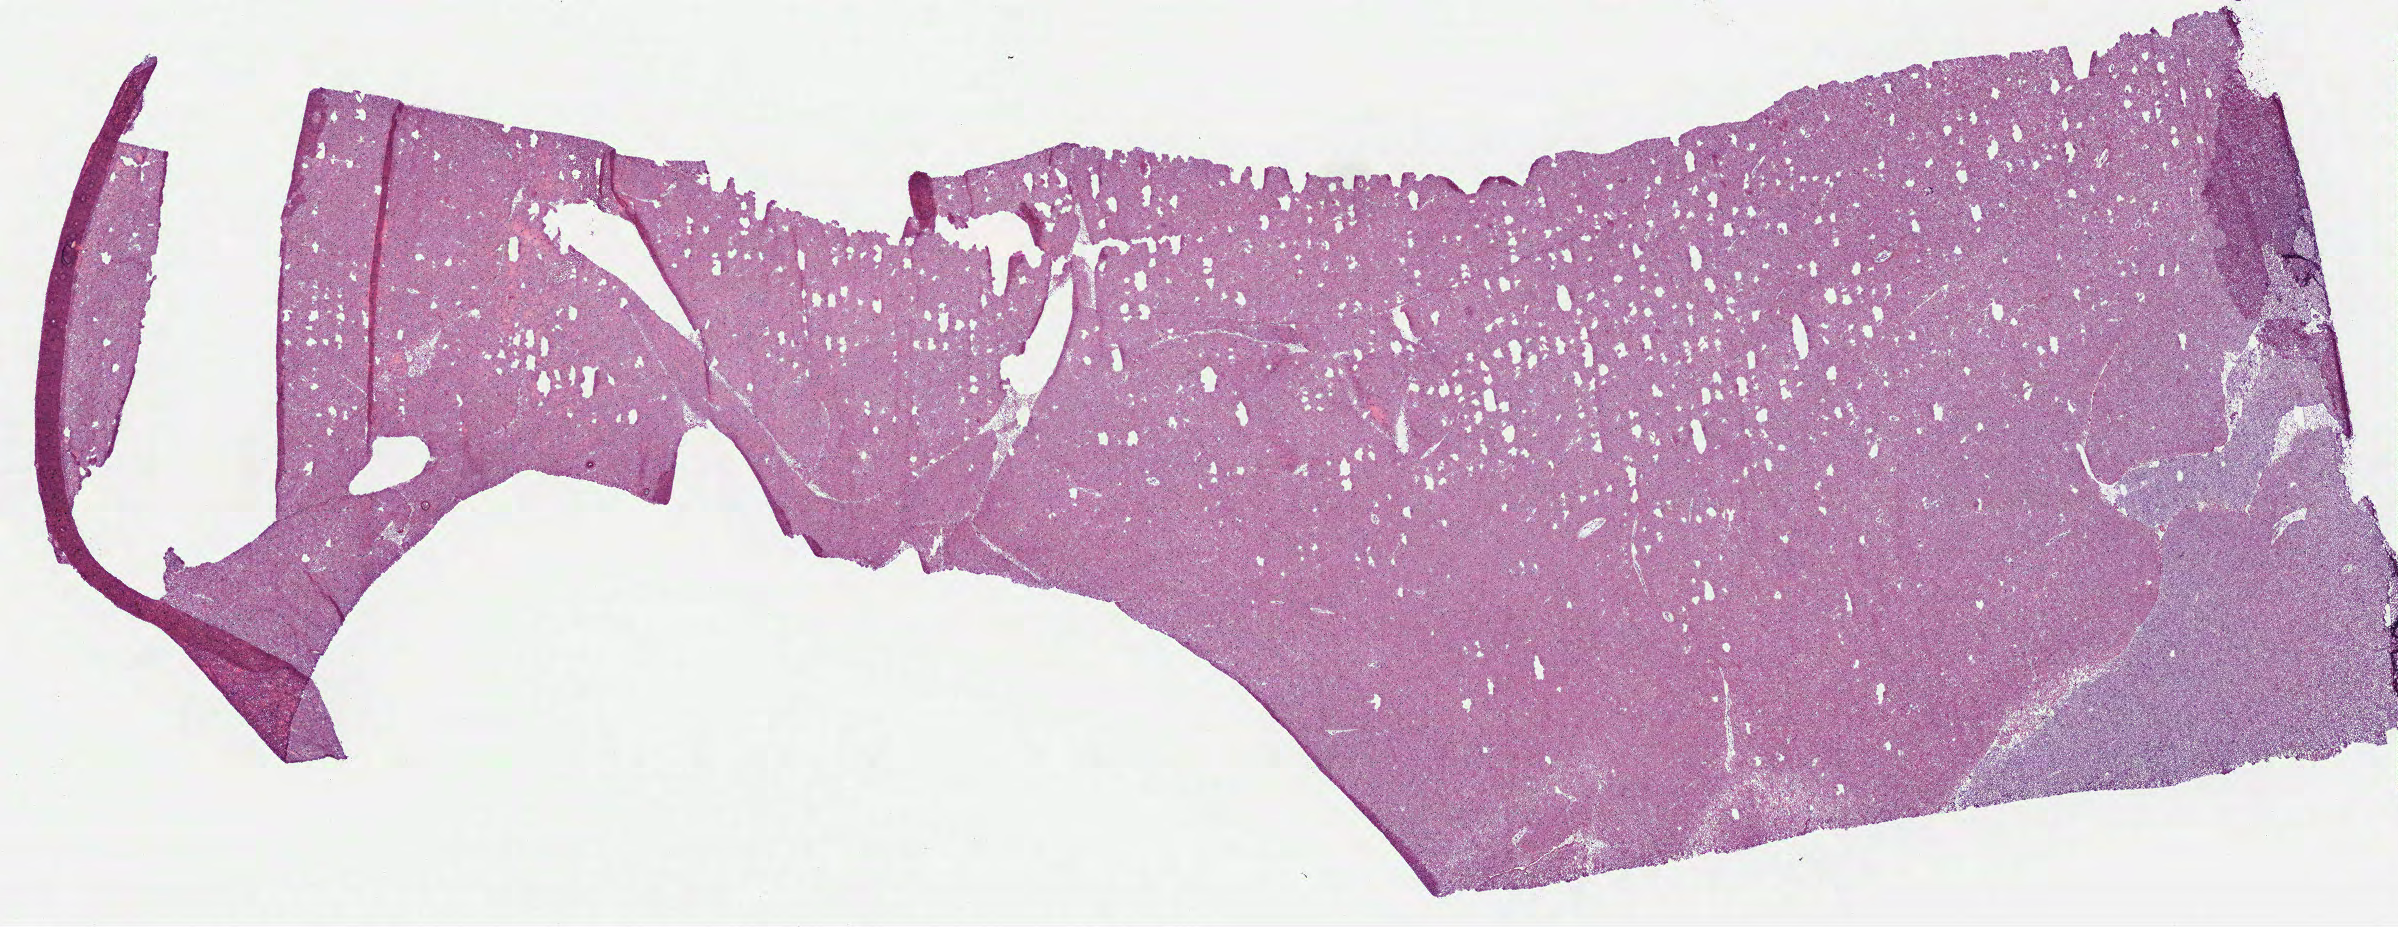
Digitized H&E-stained tissue section (whole slide), whole scanned area (about 19.3 x 7.5 mm, acquisition: 40x scan) shown as a low-resolution overview. Frozen section from the bottom of the tissue portion. Primary tumour sample from the brain. Male patient; age at initial diagnosis 40 years. Histologic grade: G3 (poorly differentiated). Slide review estimates, as recorded: tumour cells 92%, tumour nuclei 60%, normal cells 8%, stromal cells 0%, necrosis 0%.
Pathologic diagnosis: Oligodendroglioma, anaplastic.